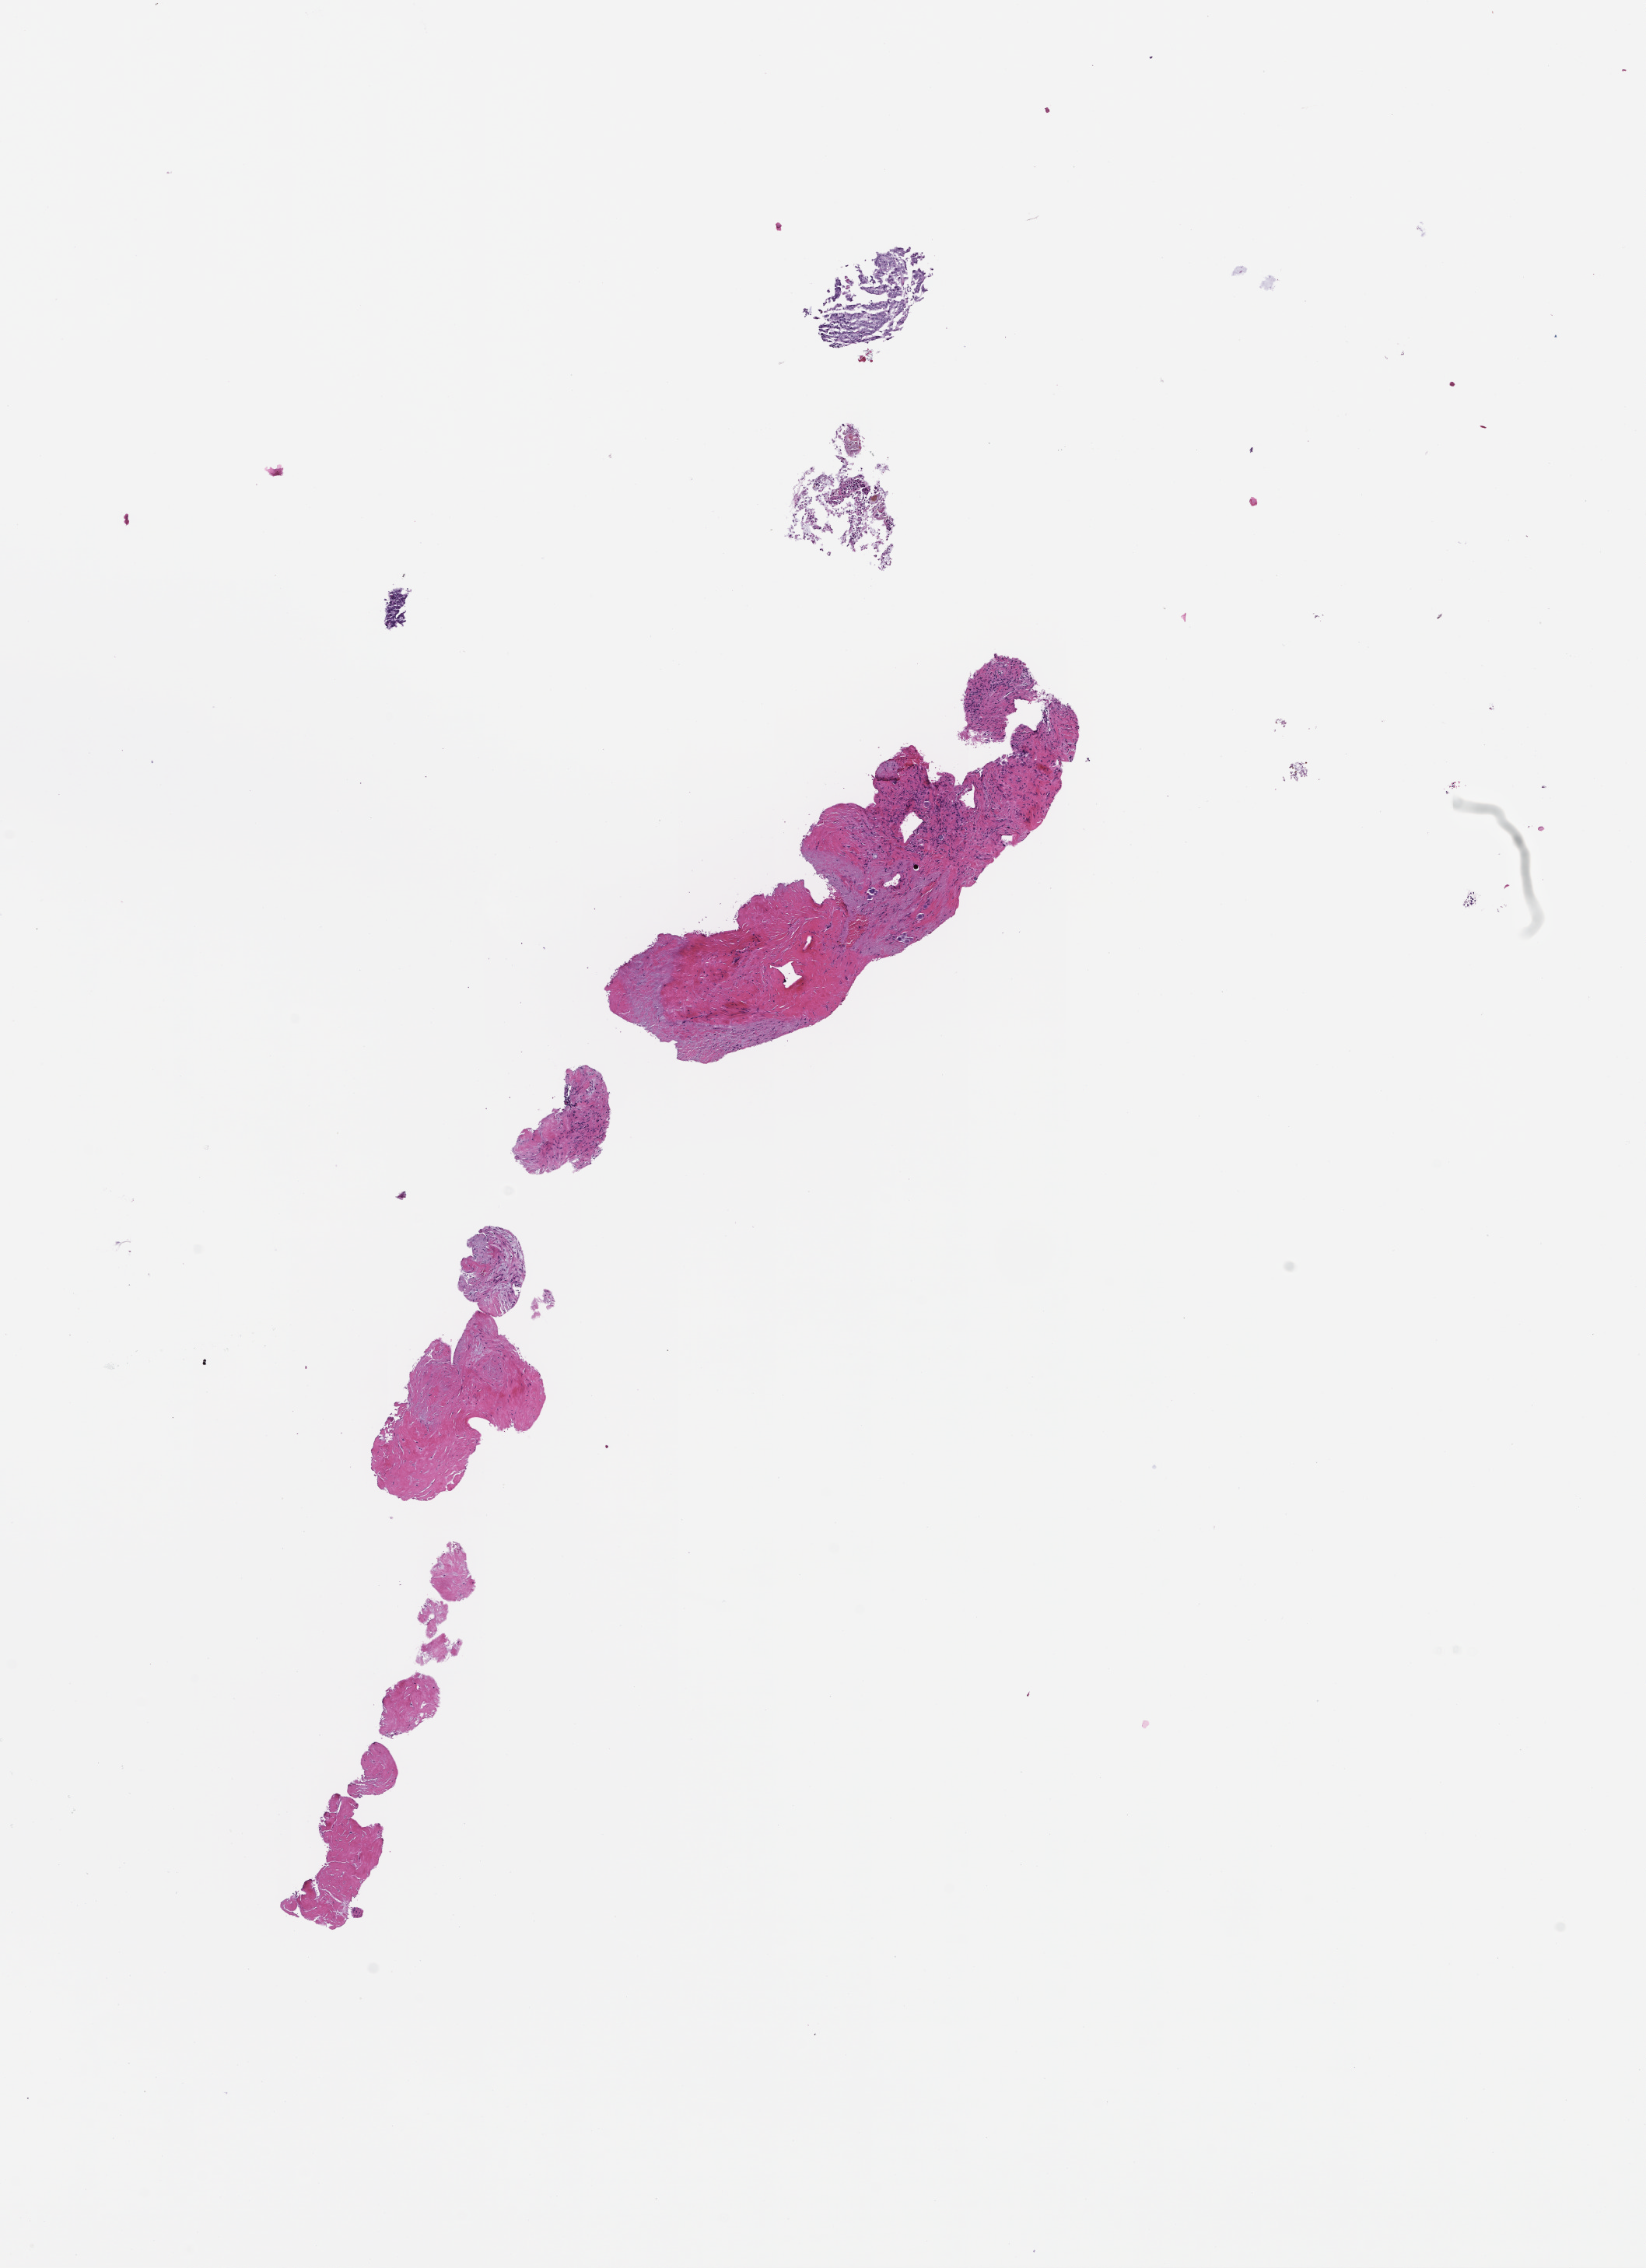
Whole-slide image, hematoxylin and eosin (H&E) stain — whole scanned area (about 8.5 x 11.8 mm) shown as a low-resolution overview; formalin-fixed, paraffin-embedded (FFPE) tissue; specimen time point: collected at disease progression. Patient sex: male.
* this section: metastatic tumor tissue
* primary diagnosis of the patient: Colorectal Carcinoma